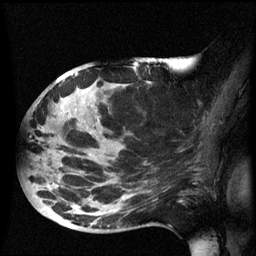
Breast MRI (dynamic contrast-enhanced), one sagittal slice. Slice 33 of 60 in the series (ordered by position). Dynamic contrast-enhanced series, image 2 of 3 at this slice position (ordered by acquisition). 1.5 T. TE 4.2 ms, TR 8.4 ms. 256 × 256 image matrix, field of view 220 × 220 mm. Female patient, age 49 years.
Outlined on this slice (semi-automatic segmentation, software-assisted and operator-edited):
- analysis volume of interest (the breast-tissue region the enhancement analysis was run in; not a lesion): bounding box [x1, y1, x2, y2] px = [24, 72, 185, 233]
- tumour enhancement mask (voxels above the 70 % enhancement threshold inside the analysis volume of interest): [76, 74, 78, 77]